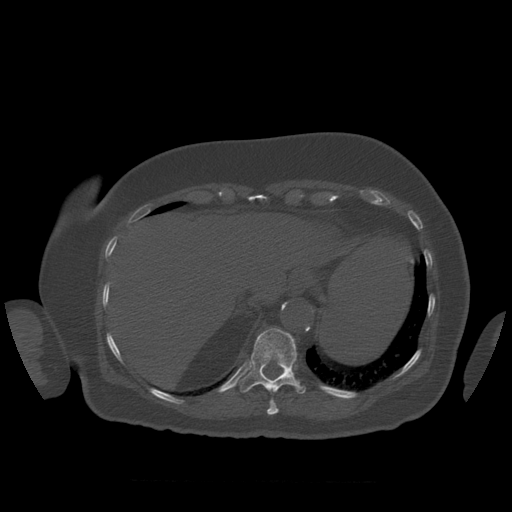
CT including the spine, one axial slice. Slice 324 of 399 in the series (ordered by position). Reconstruction kernel STANDARD. 120 kVp. Bone window (W 1800 / L 400 HU). 1.25 mm slice thickness. 512 × 512 image matrix, field of view 404 × 404 mm. Patient age 81 years. From the clinical record (not read from this slice): primary cancer: renal; vertebrae with lytic lesions (as recorded): L1.
Annotated regions visible in this slice (semi-automatic segmentation, software-assisted and operator-edited):
- T10 vertebra: bounding box (x1, y1, x2, y2) in pixels: (267, 400, 279, 415)
- T11 vertebra: (240, 328, 306, 394)